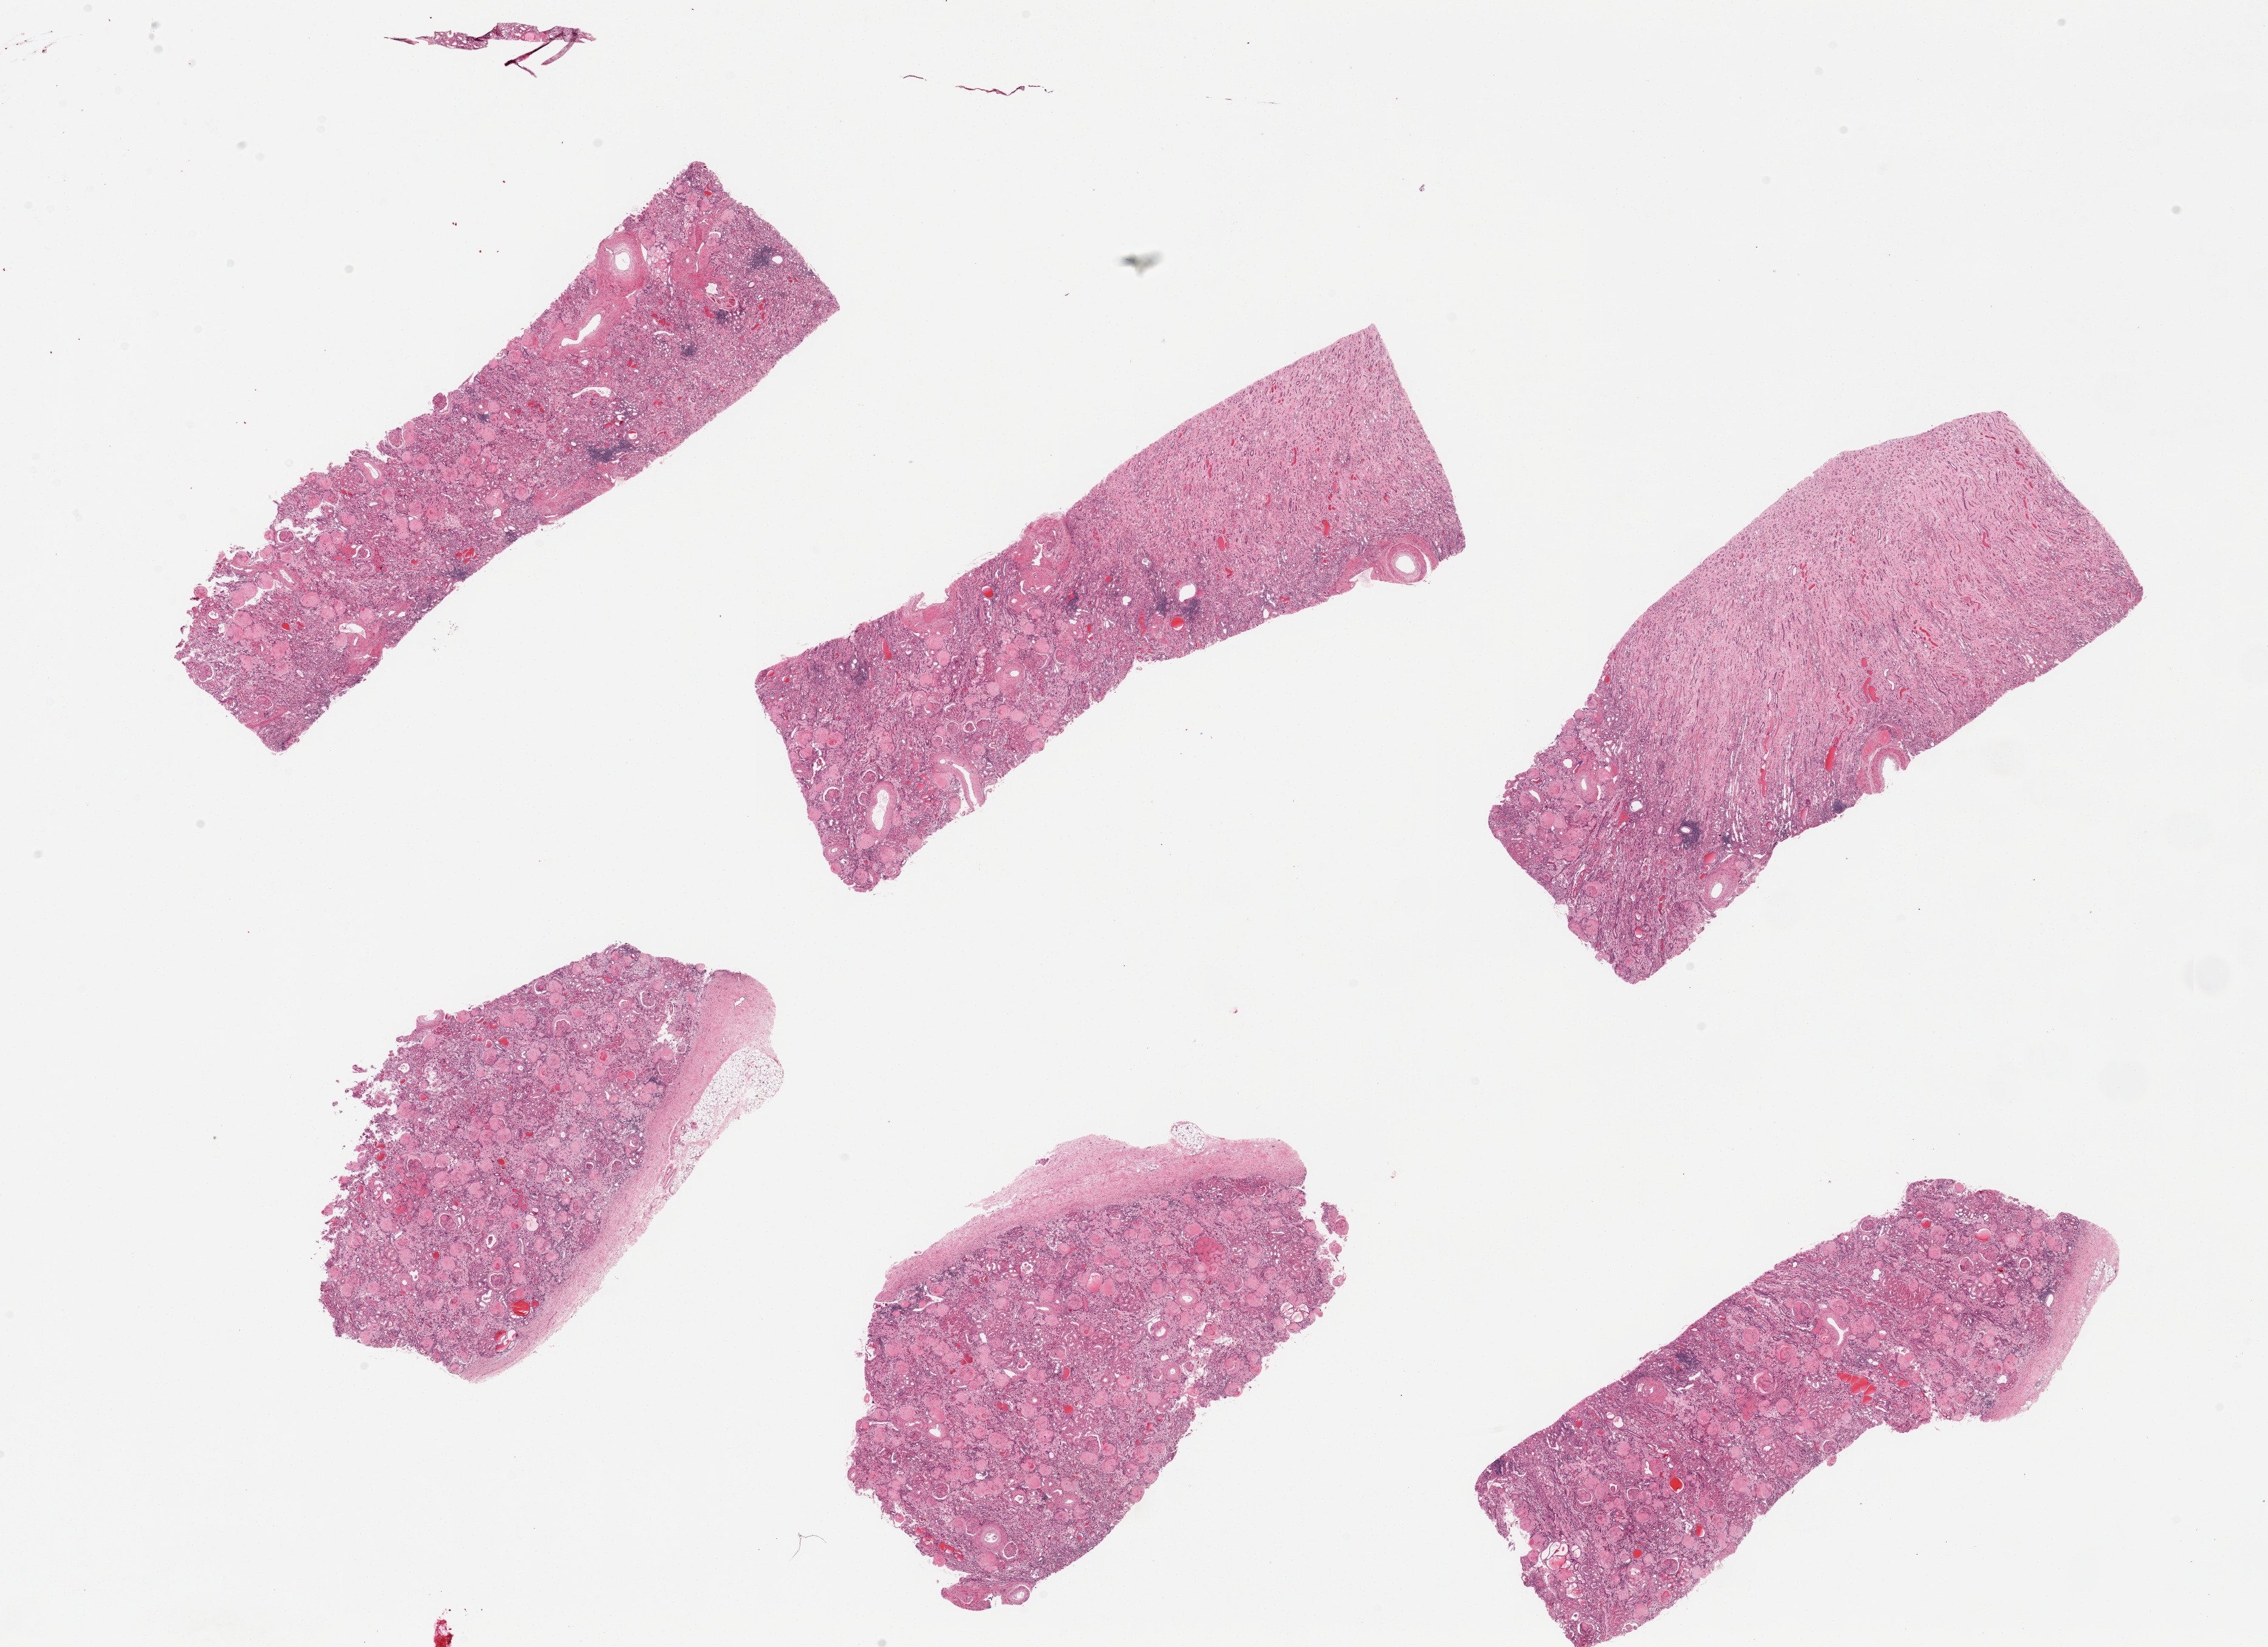
Hematoxylin and eosin (H&E) whole-slide image — whole scanned area (about 29.5 x 21.4 mm, acquisition: 20x scan) shown as a low-resolution overview; PAXgene-fixed, paraffin-embedded tissue; section of renal cortex (target tissue); donor tissue sample. Donor: female.
- review note (as recorded): 6 pieces, all sections with glomeruli, marked diffuse glomerular sclerosis